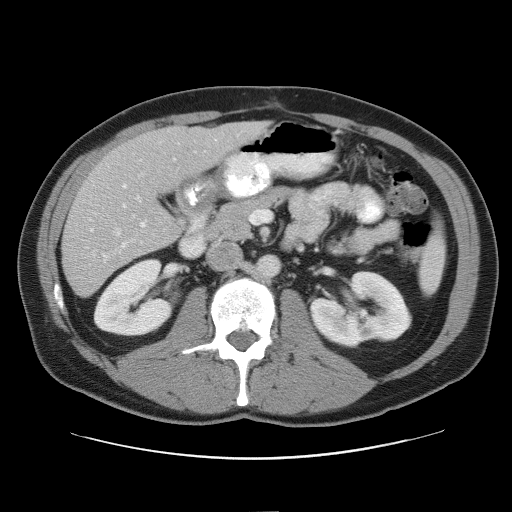
Contrast-enhanced abdominal CT, one axial slice. Position 27 of 52 along the scan axis. Intravenous contrast given. Soft-tissue window (W 400 / L 40 HU). 5 mm slice thickness. 512 × 512 image matrix, field of view 393 × 393 mm. Male patient, age 70 years. From the clinical record (not read from this slice): diagnosis: colorectal cancer liver metastases, imaged before liver resection; multiple liver metastases: yes; largest metastasis: 4 cm; chemotherapy before resection: yes.
Annotated regions visible in this slice (manually delineated by an expert):
- hepatic veins: bounding box (x1, y1, x2, y2) in pixels: (88, 172, 145, 263)
- liver: (63, 122, 265, 297)
- planned liver remnant (the part of the liver to remain after resection): (118, 122, 264, 192)
- portal vein (with intrahepatic branches): (122, 184, 147, 246)